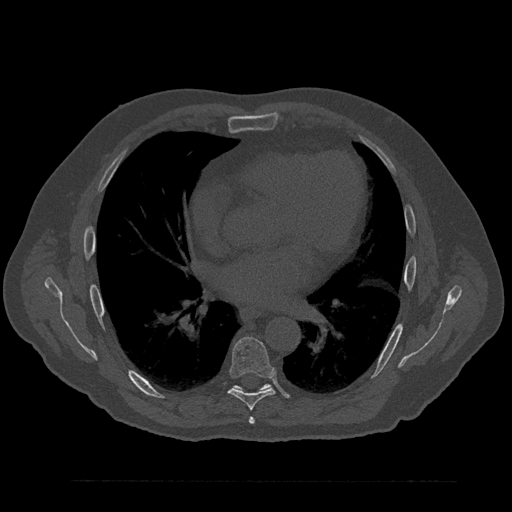
CT including the spine, one axial slice. Position 497 of 797 along the scan axis. Reconstruction kernel Br40s/3. Bone window (W 1800 / L 400 HU). 512 × 512 image matrix, field of view 430 × 430 mm. Patient: male, 61 years. From the clinical record (not read from this slice): primary cancer: prostate.
Outlined on this slice (semi-automatically segmented with operator editing):
- T6 vertebra: bounding box <249,417,255,424> (left, top, right, bottom; pixels)
- T7 vertebra: <228,337,275,410>
- T8 vertebra: <233,384,271,391>